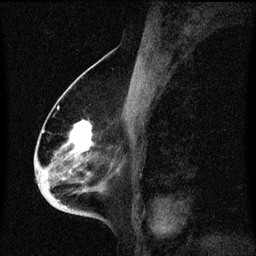
Breast MRI (dynamic contrast-enhanced), one sagittal slice; position 35 of 60 along the scan axis; dynamic contrast-enhanced series, image 2 of 3 at this slice position (ordered by acquisition); 1.5 T; TE 4.2 ms, TR 8.4 ms; 2 mm slice thickness; 256 × 256 image matrix. Female patient, age 68 years. Case-level facts recorded for this patient, not image findings: setting: breast cancer imaged before/during neoadjuvant chemotherapy; receptor status: triple-negative.
Annotated regions visible in this slice (semi-automatic segmentation, software-assisted and operator-edited):
- analysis volume of interest (the breast-tissue region the enhancement analysis was run in; not a lesion): bounding box [x1, y1, x2, y2] px = [36, 96, 113, 213]
- tumour enhancement mask (voxels above the 70 % enhancement threshold inside the analysis volume of interest): [66, 120, 92, 191]